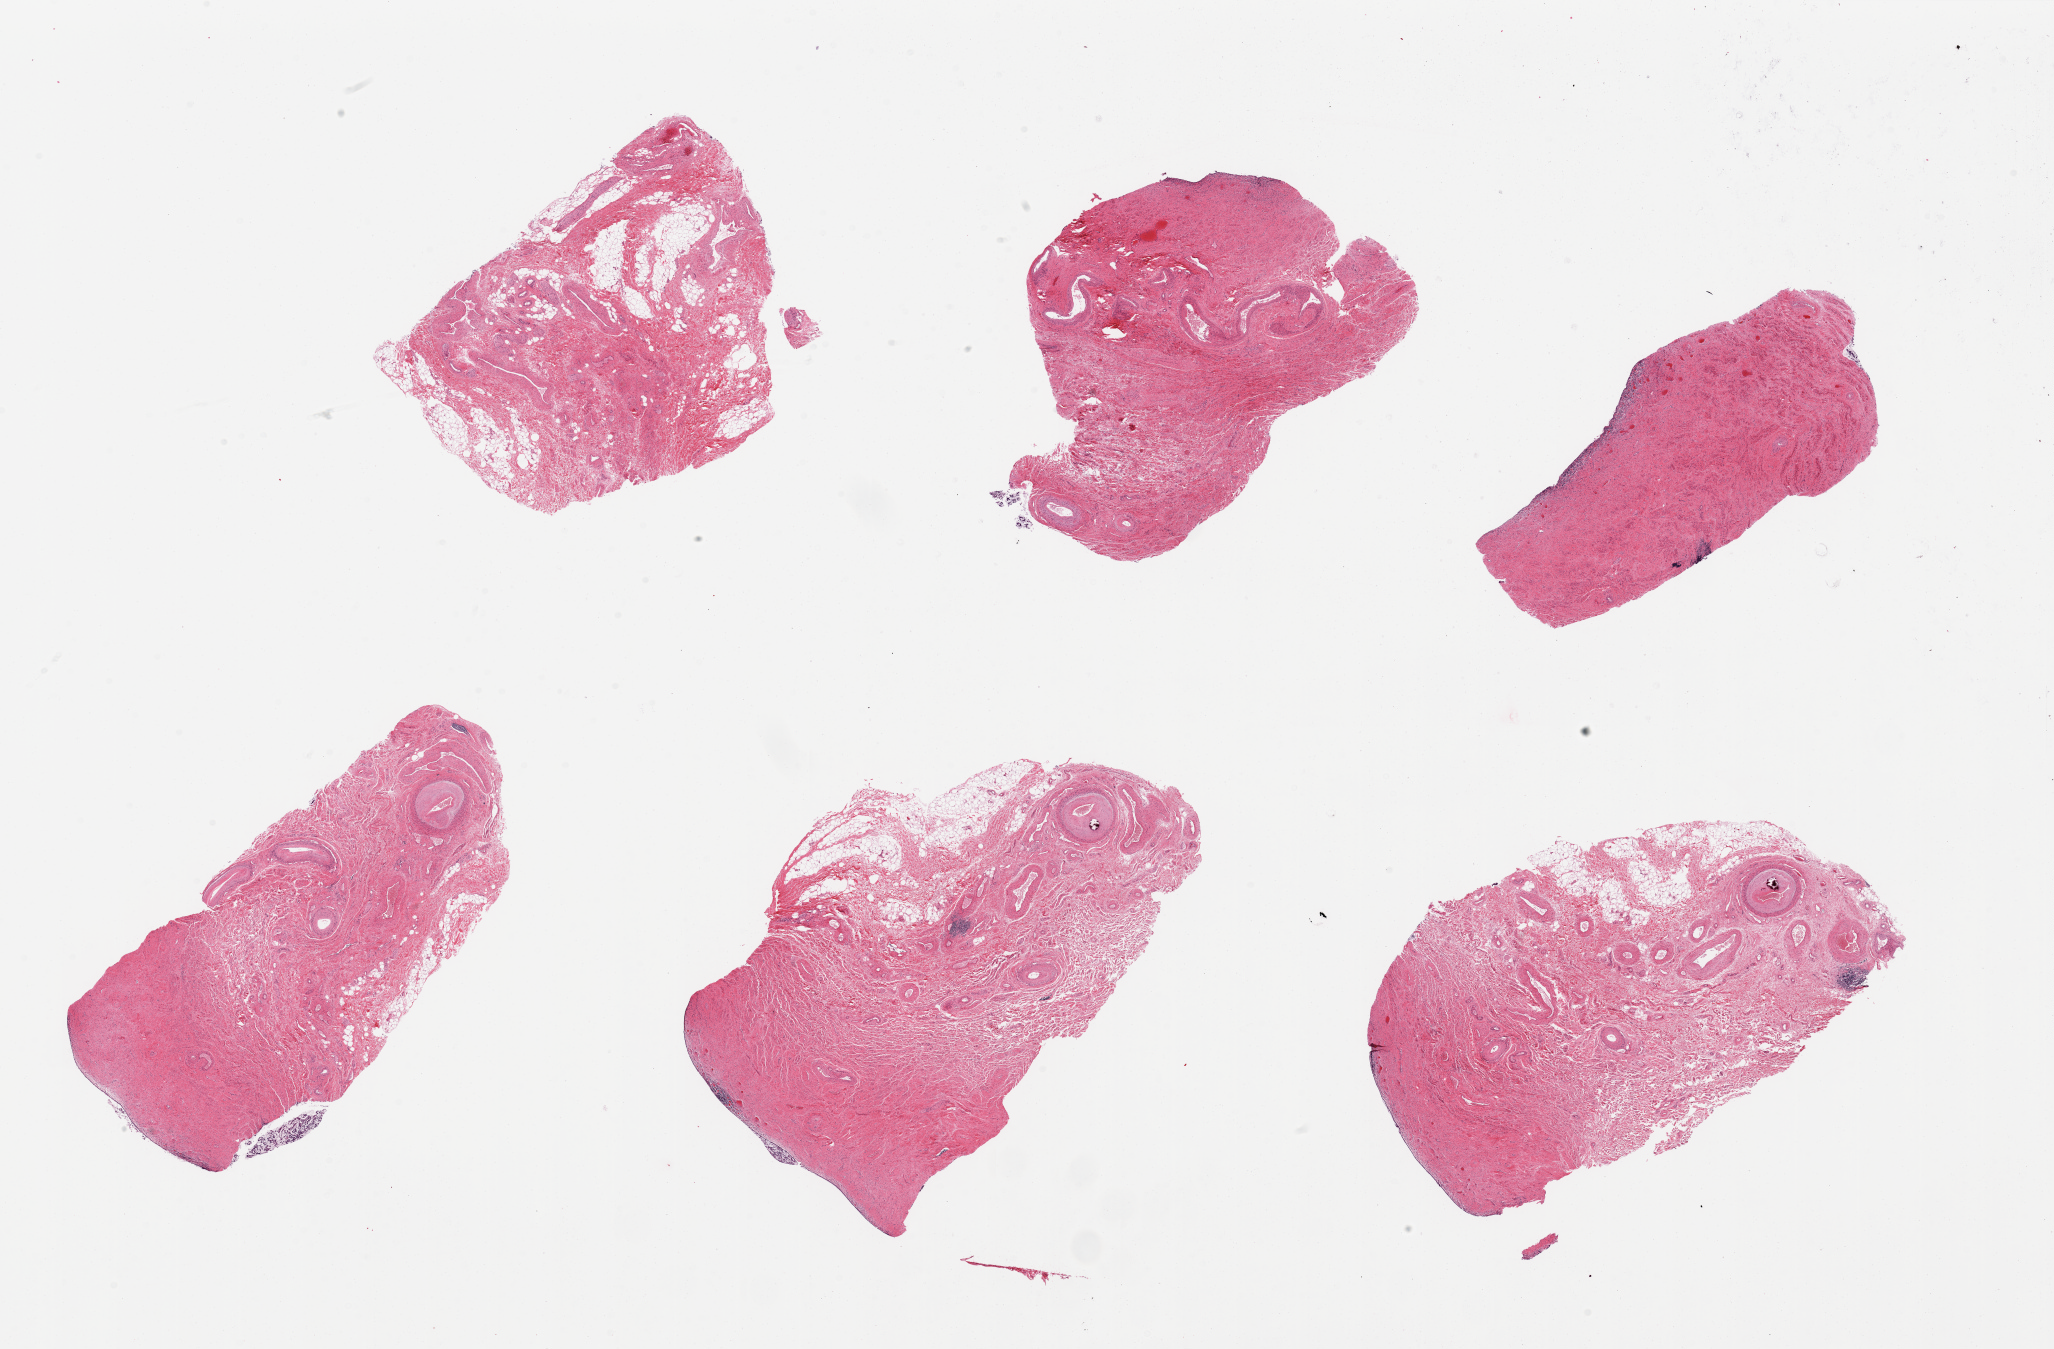
Digitized hematoxylin and eosin (H&E)-stained section — low-resolution overview of the scanned area, about 32.5 x 21.3 mm, PAXgene-fixed paraffin-embedded (PFPE) section, sampled site (target tissue): vagina, donor tissue sample. Donor: female.
• pathologist's review note for this sample: 6 pieces; mucosa largely sloughed